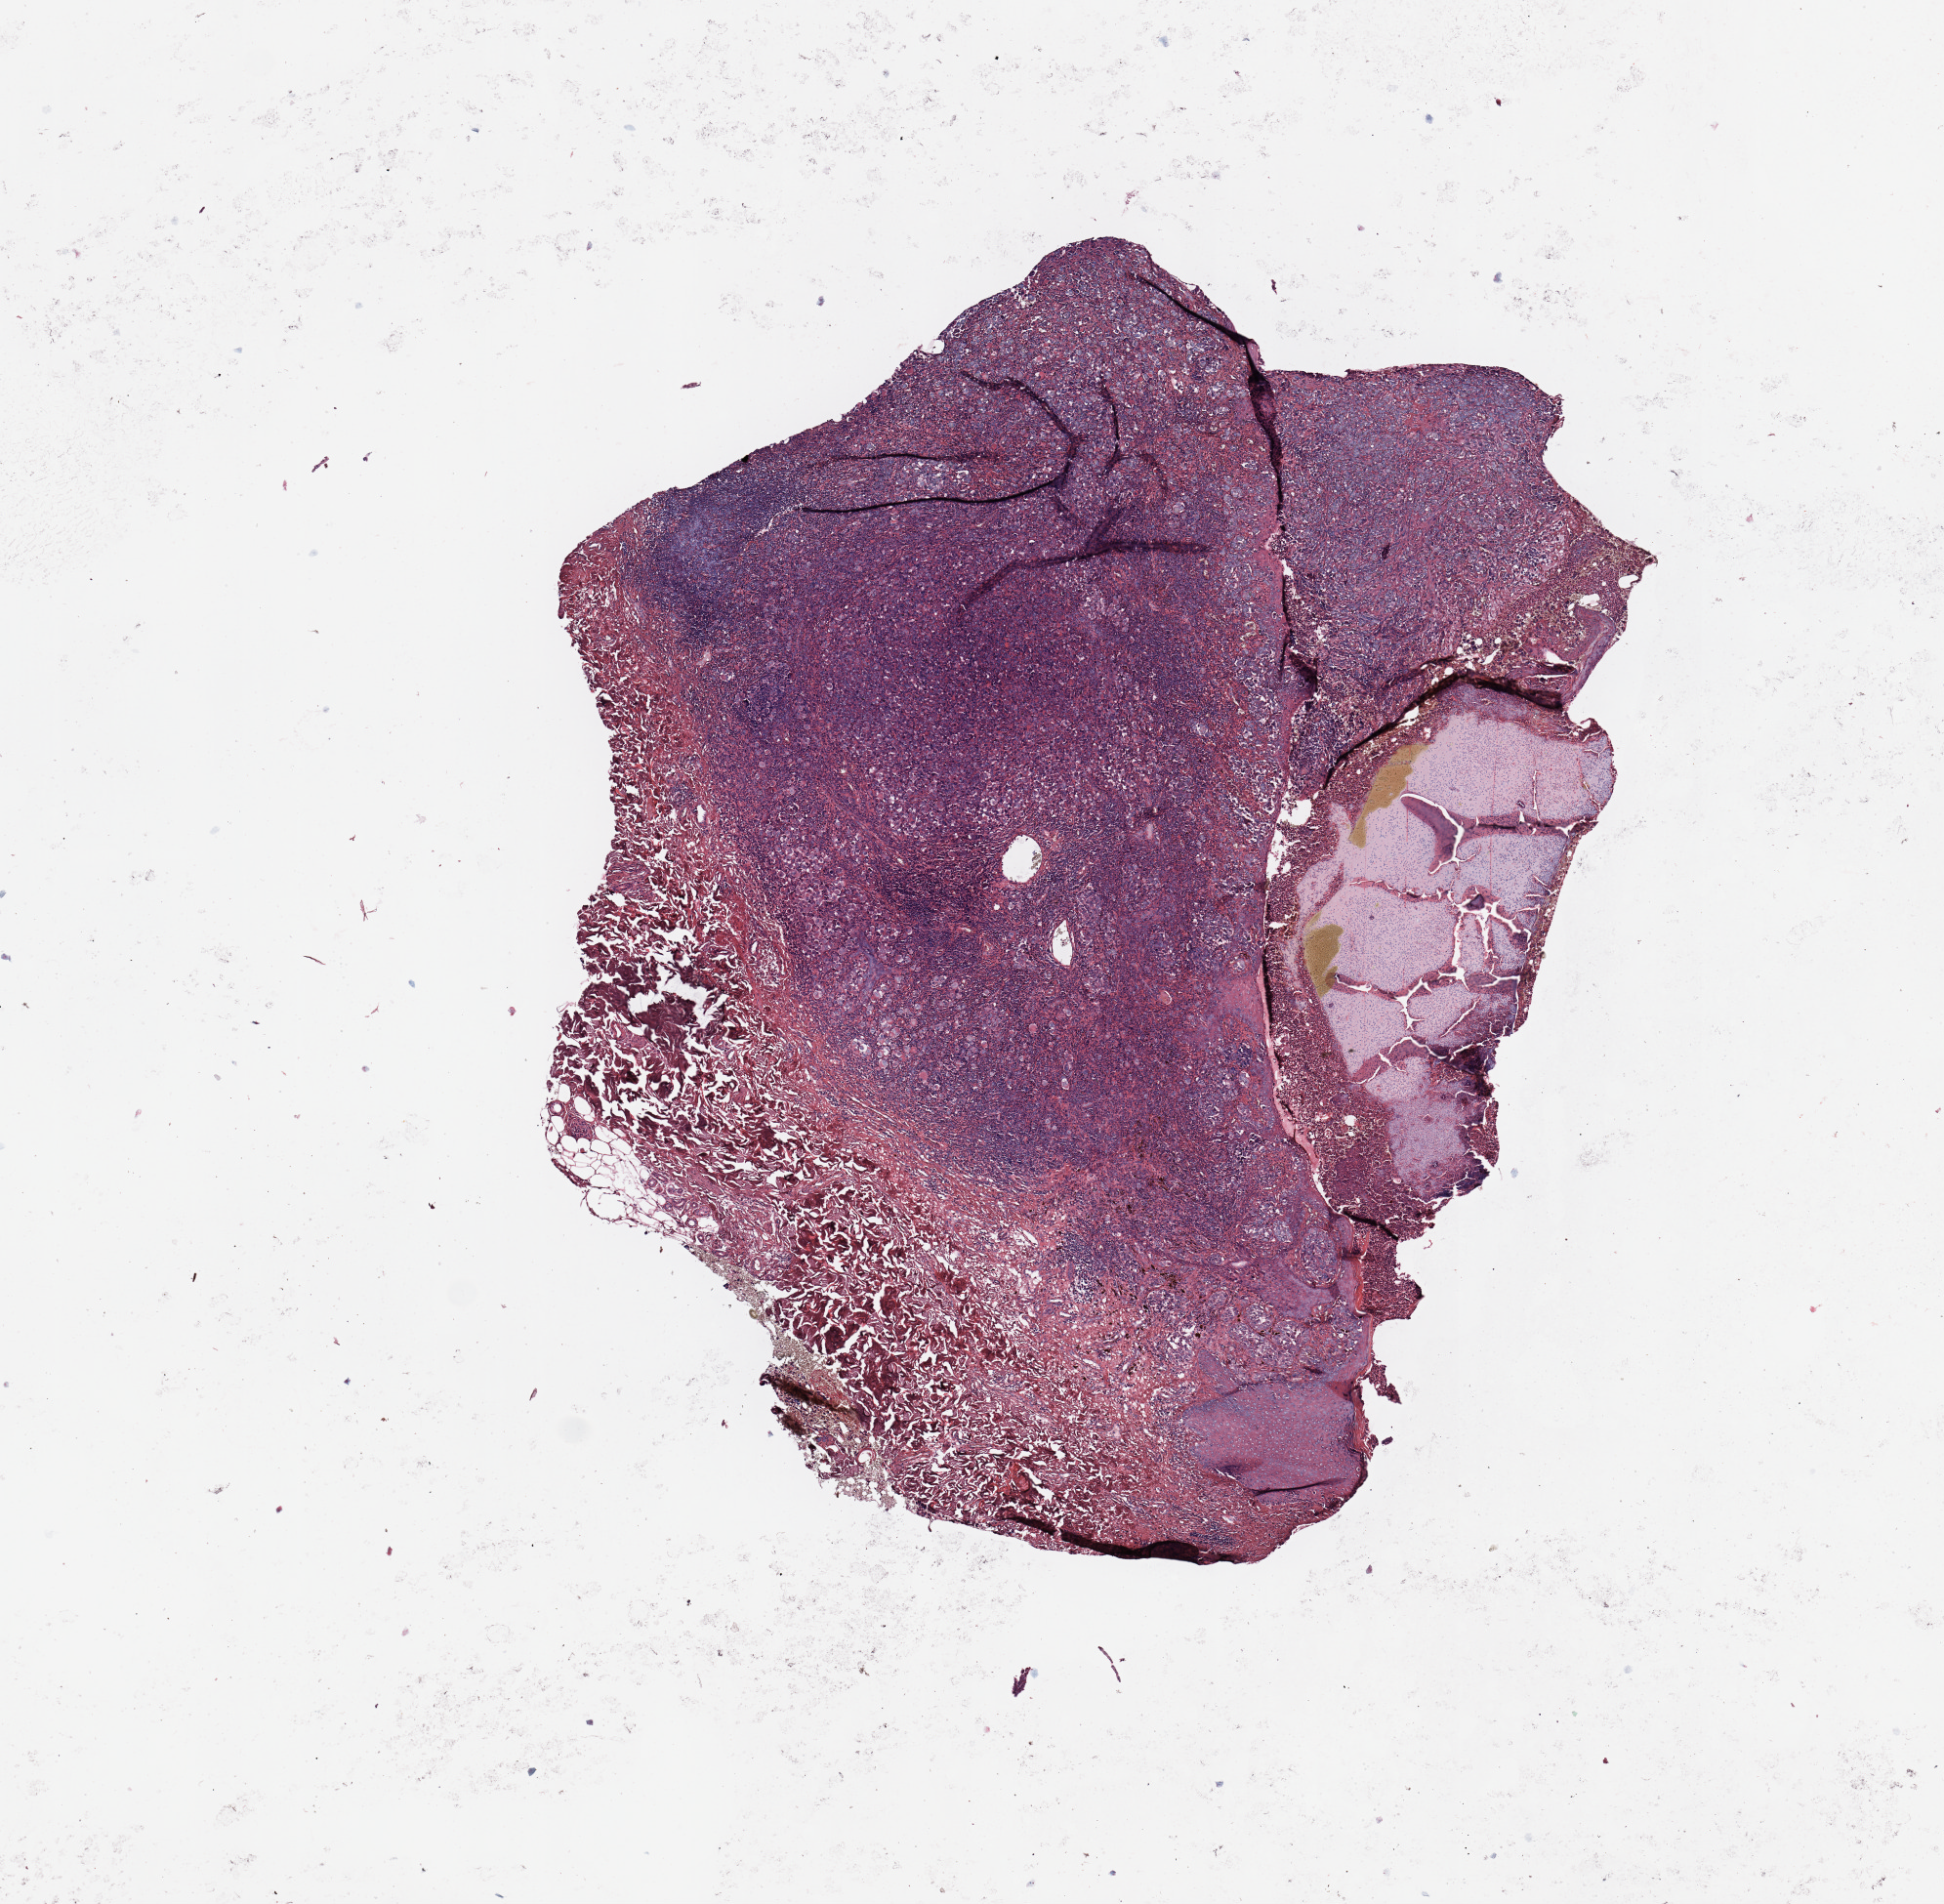
Digitized Hematoxylin and eosin (H&E) stained tissue section (whole slide) — whole scanned area (about 7.9 x 7.7 mm) shown as a low-resolution overview; tumour tissue sample, sampled site: trunk. 83-year-old male patient. Pathologist review of this section (percent, as recorded): tumour nuclei 80%, necrosis 0%.
* AJCC pathologic stage: IIB
* histologic diagnosis: Malignant melanoma, NOS
* primary tumour site (as recorded): trunk